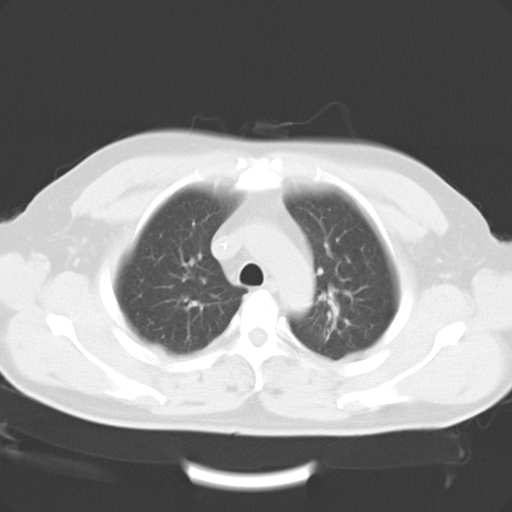
Chest CT, one axial slice; position 15 of 20 along the scan axis; reconstruction kernel B40f; lung window (W 1500 / L -600 HU); 10 mm slice thickness; 512 × 512 image matrix, field of view 362 × 362 mm. Patient: male, 45 years. From the clinical record (not read from this slice): clinical TNM (as recorded): T2 N0 M0.
Outlined on this slice (bounding box drawn by a radiologist):
- lung tumour (recorded histology: adenocarcinoma): bounding box <311,282,366,340> (left, top, right, bottom; pixels)